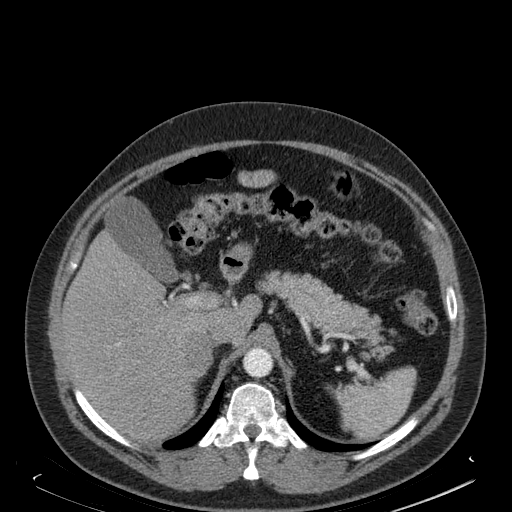
Contrast-enhanced abdominal CT, one axial slice; slice 128 of 181 in the series (ordered by position); soft-tissue window (W 400 / L 40 HU); 1.5 mm slice thickness; 512 × 512 image matrix, field of view 405 × 405 mm. Male patient. From the clinical record (not read from this slice): diagnosis: adrenocortical carcinoma; tumour side: right adrenal; tumour size at pathology: 7.5 cm; Ki-67 index: 25 %; stage (as recorded): 4.
Outlined on this slice (semi-automatically segmented with operator editing):
- mass: box from (x=183, y=333) to (x=211, y=376) px